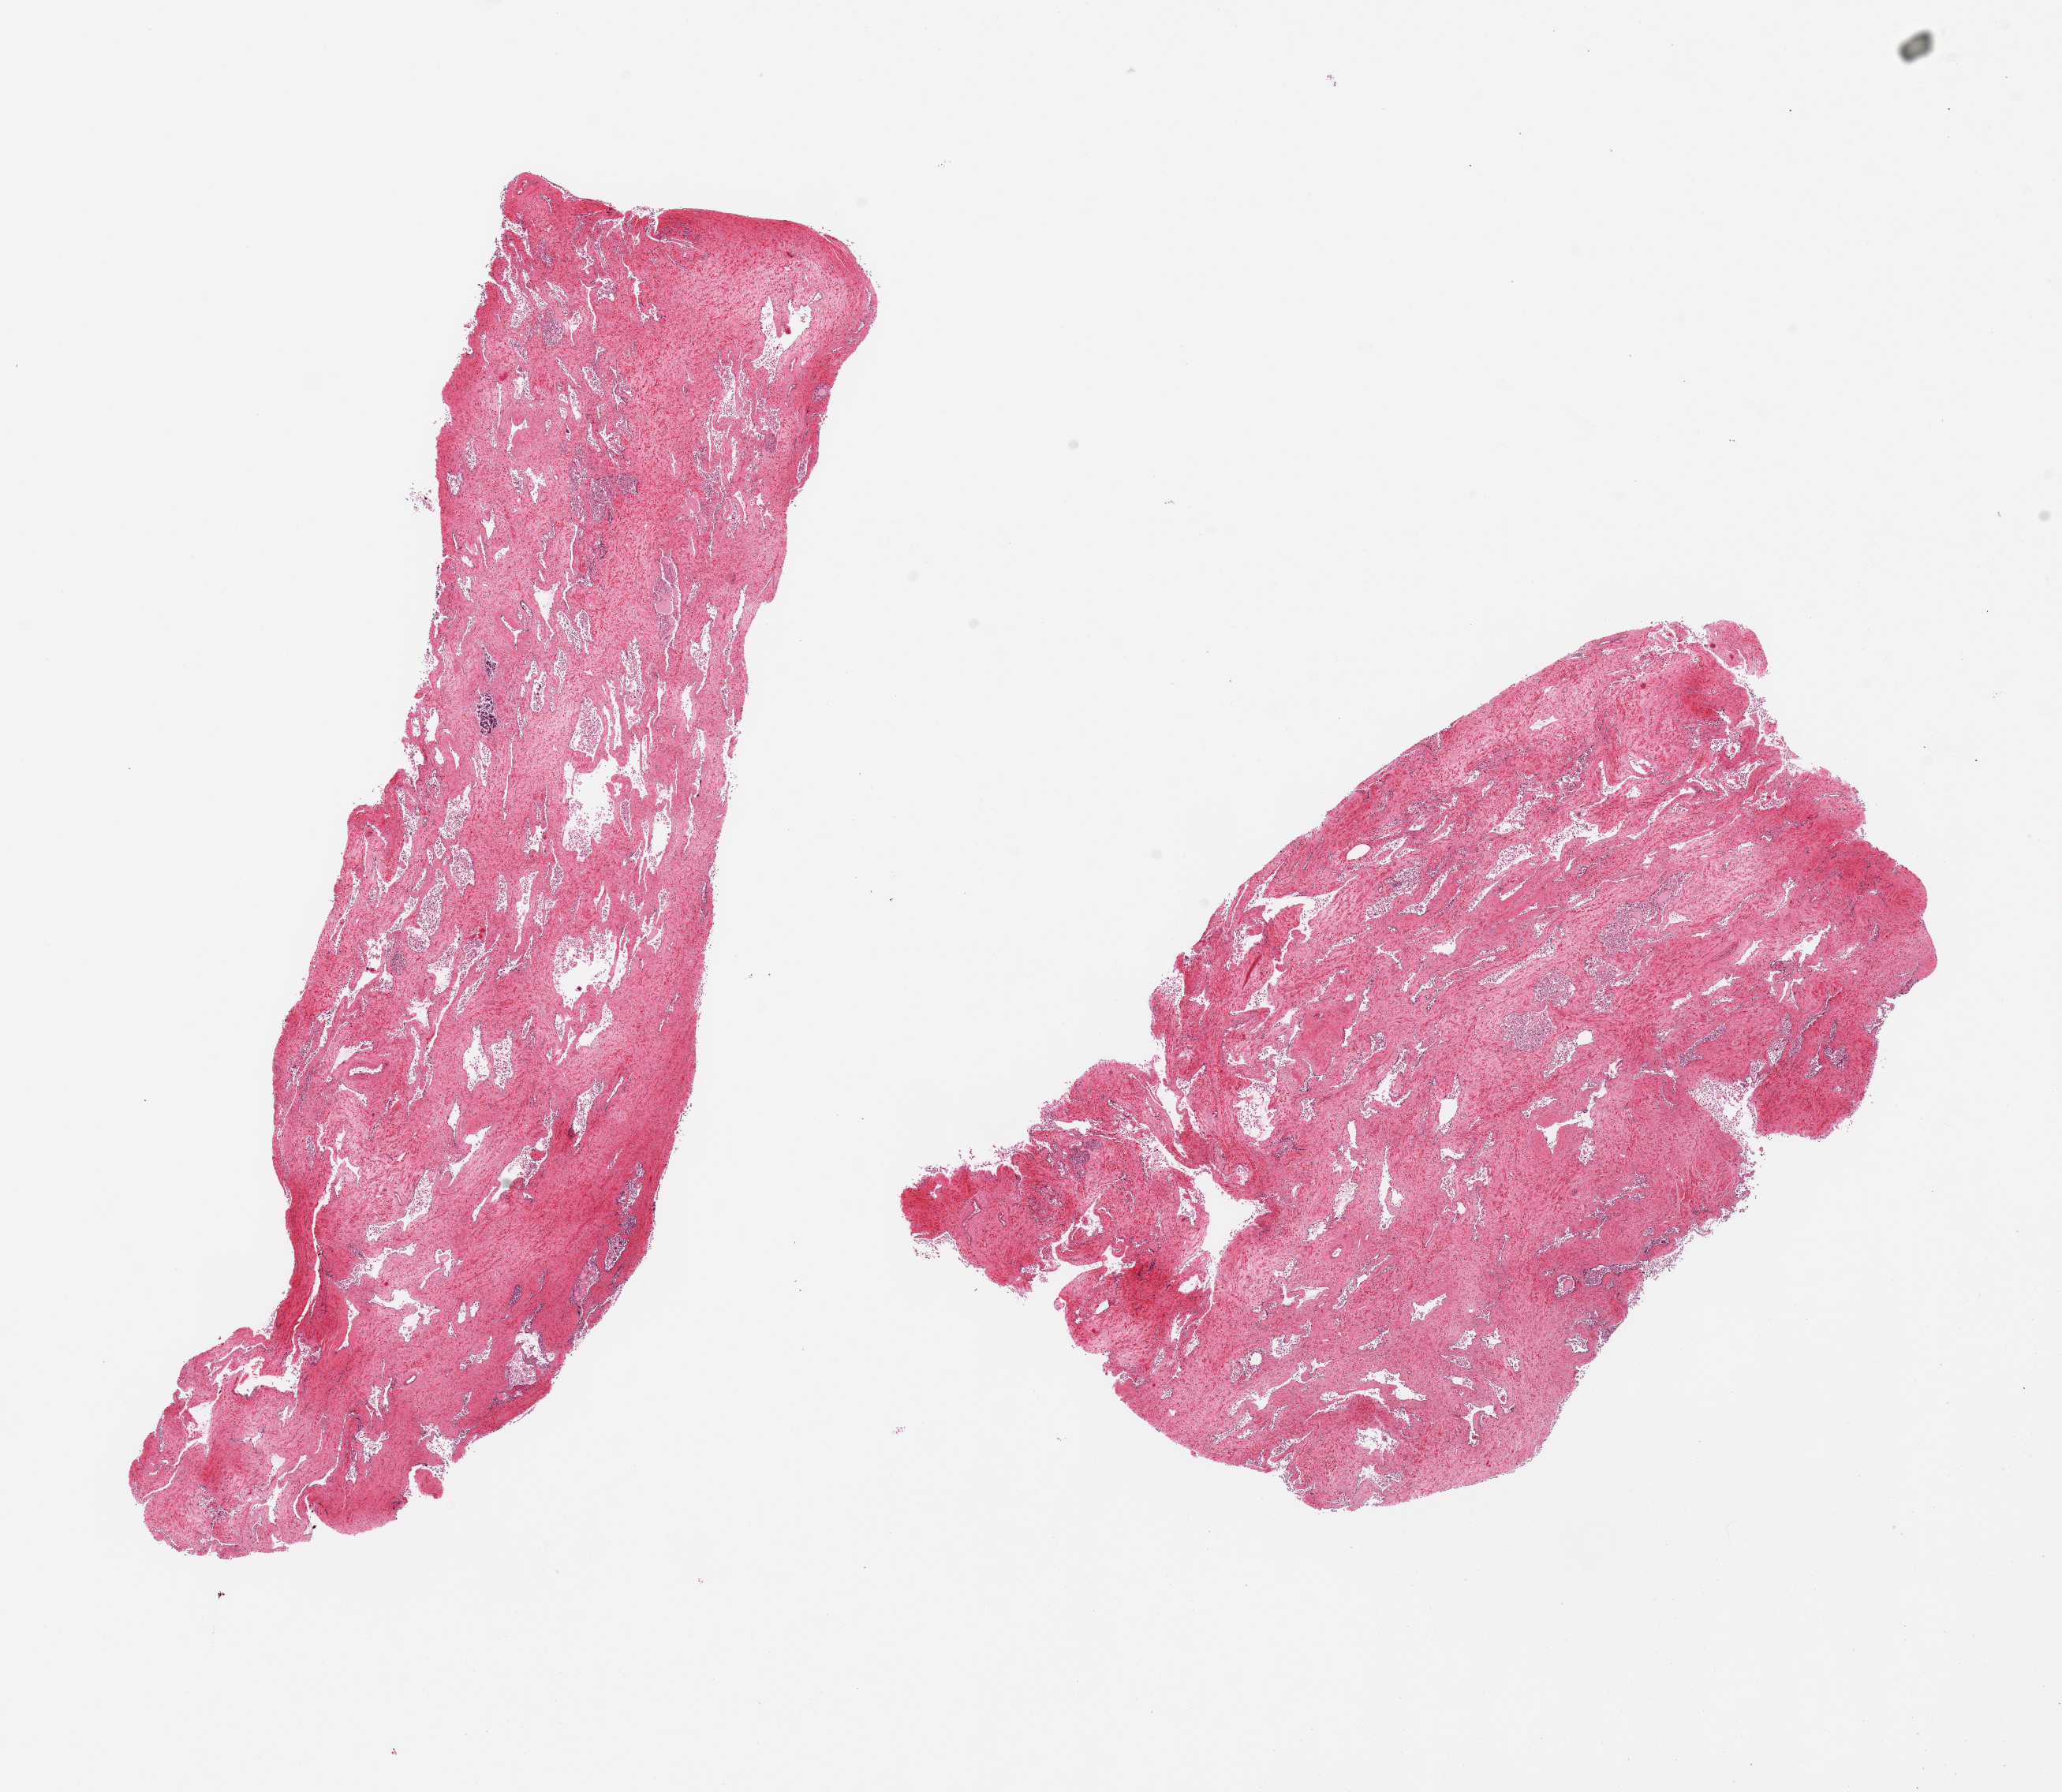
H&E whole-slide image, brightfield, whole scanned area (about 20.7 x 18.0 mm) shown as a low-resolution overview; PAXgene-fixed, paraffin-embedded tissue; target tissue: prostate; donor tissue sample. Male donor.
Review note (as recorded): 2 pieces; glands totally autolyzed; fibromuscular stroma = 1.